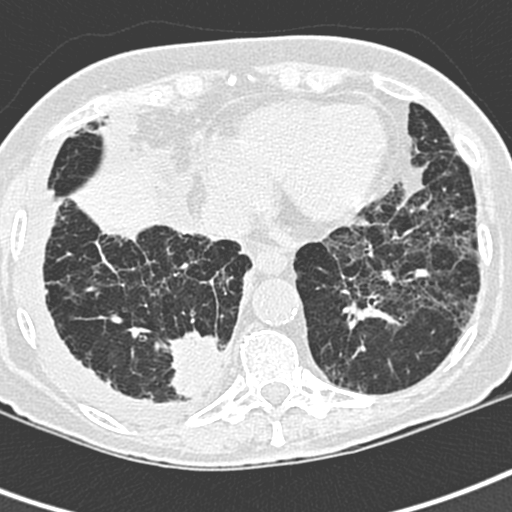
Low-dose screening chest CT, one axial slice. Slice 81 of 220 in the series (ordered by position). 120 kVp. Lung window (W 1500 / L -600 HU). 1.3 mm slice thickness. 512 × 512 image matrix, field of view 288 × 288 mm.
Structures marked on this image (expert manual segmentation):
- lesion 1 (tumor, lower lobe of right lung): bounding box <165,330,225,399> (left, top, right, bottom; pixels)